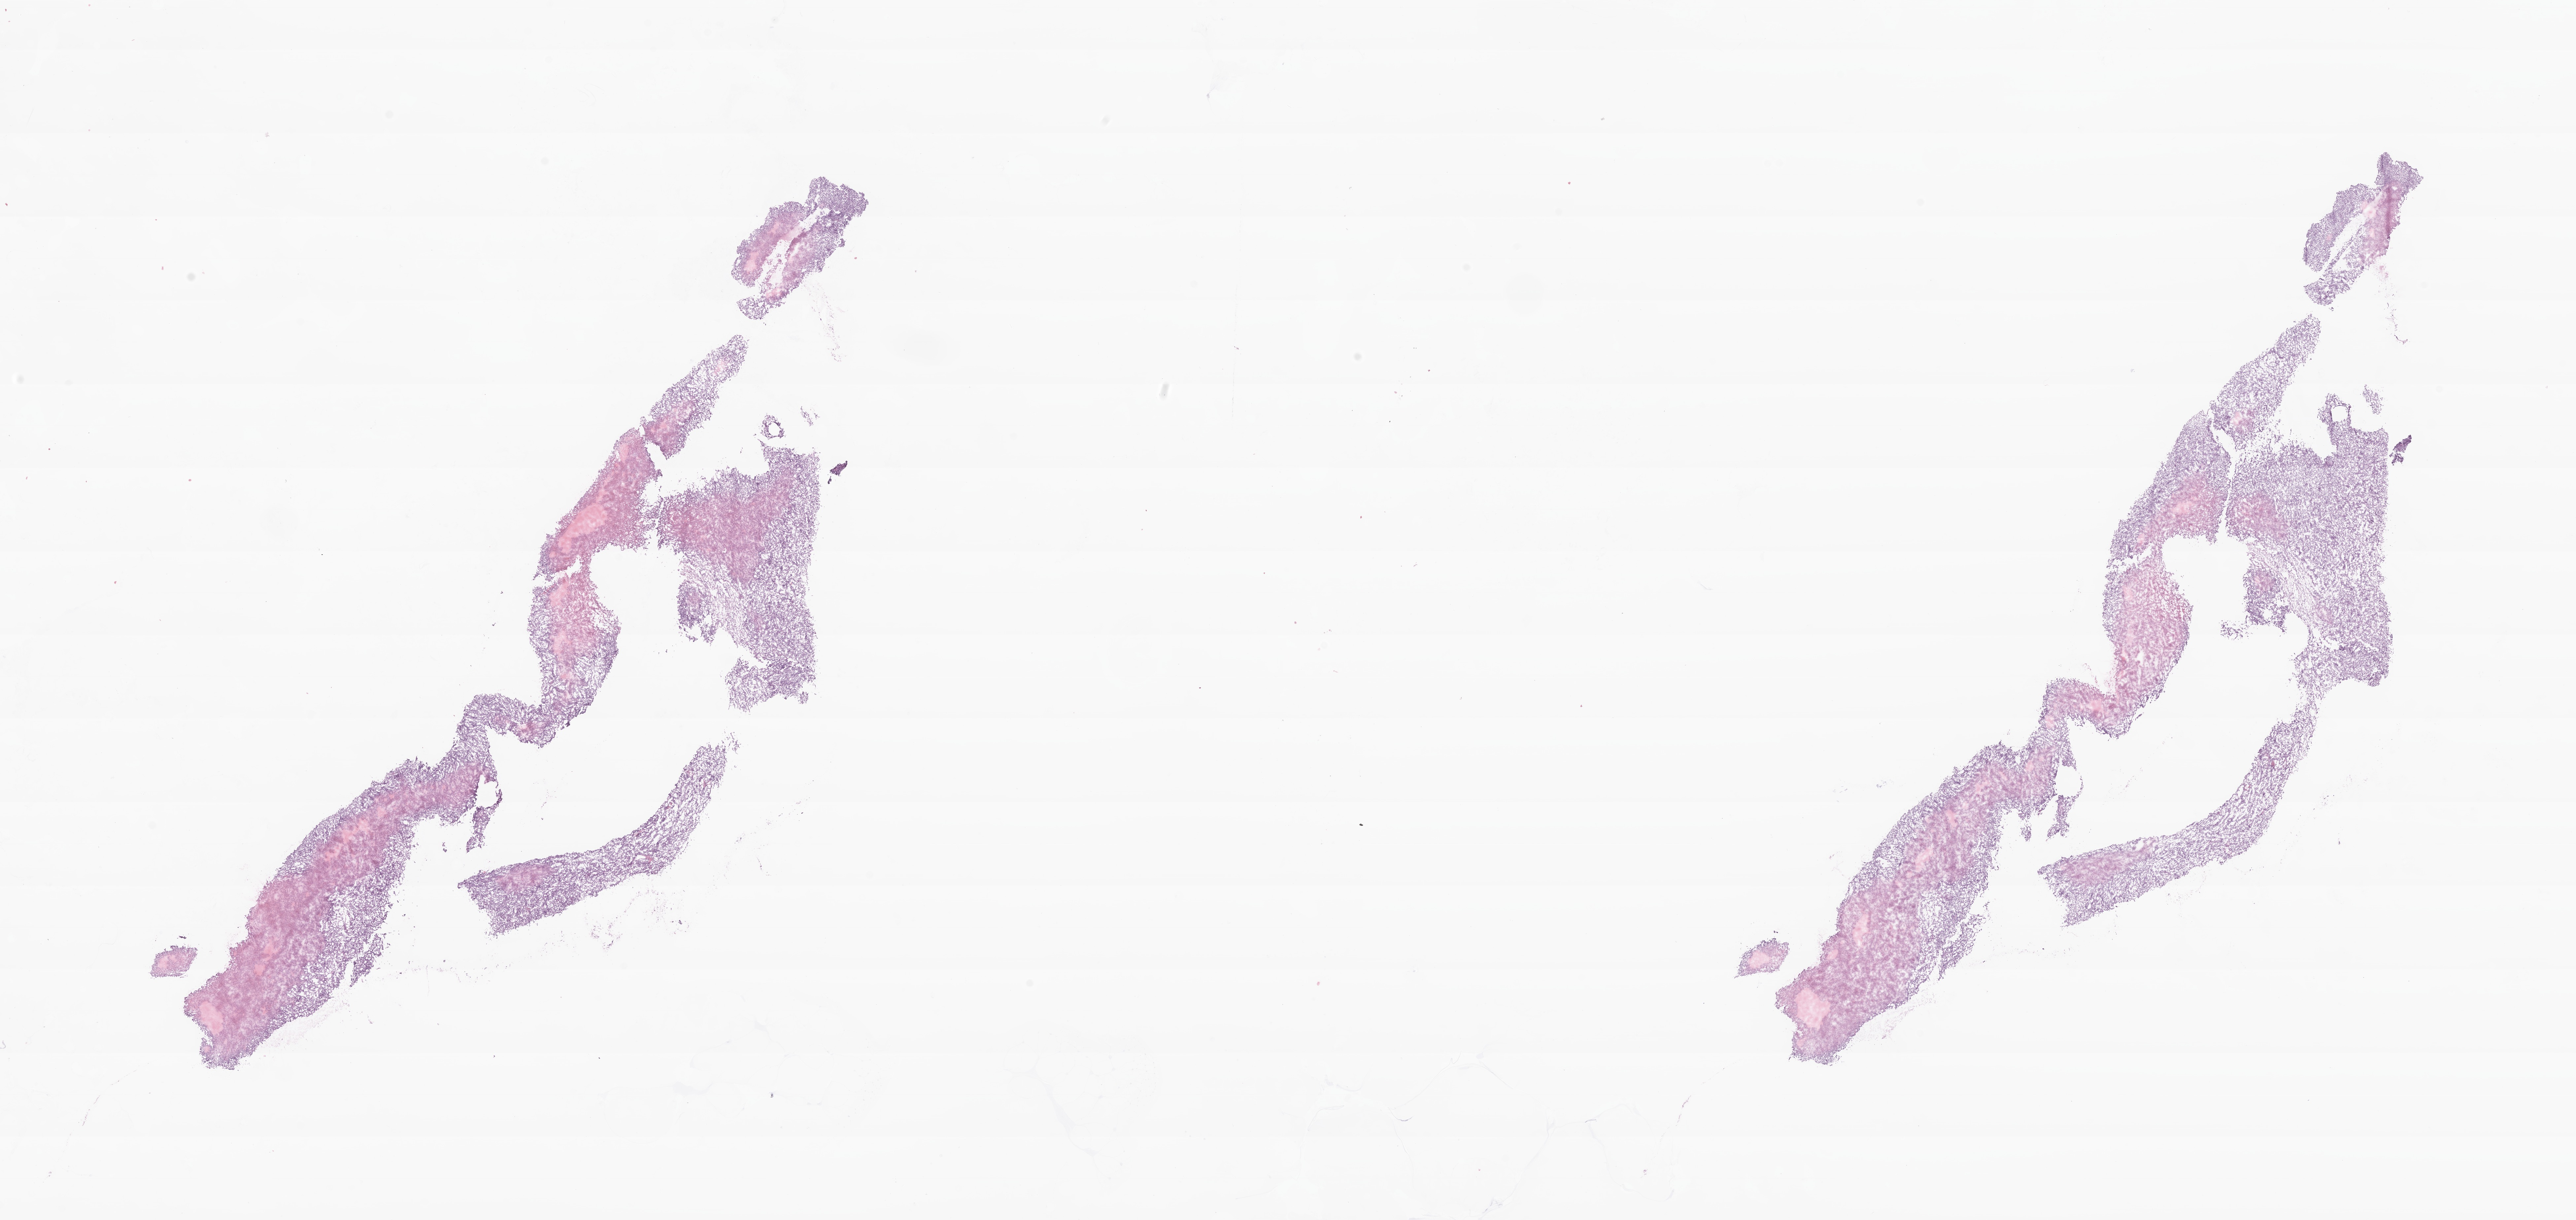
H&E whole-slide image of tumor tissue from the ovary, whole scanned area (about 32.8 x 15.5 mm) shown as a low-resolution overview; frozen section. Patient: female, age 180 months.
* recorded diagnosis: Sertoli cell tumor, NOS